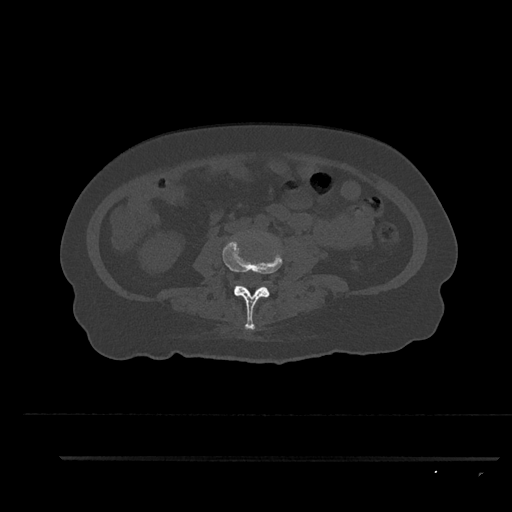
CT including the spine, one axial slice; slice 68 of 797 in the series (ordered by position); reconstruction kernel Br40s/3; bone window (W 1800 / L 400 HU); 0.5 mm slice thickness; 512 × 512 image matrix, field of view 408 × 408 mm. Patient: female, 44 years. From the clinical record (not read from this slice): primary cancer: renal.
Structures marked on this image (semi-automatic segmentation, software-assisted and operator-edited):
- L3 vertebra: box from (x=222, y=237) to (x=282, y=330) px
- L4 vertebra: (x=270, y=285)–(x=276, y=292)